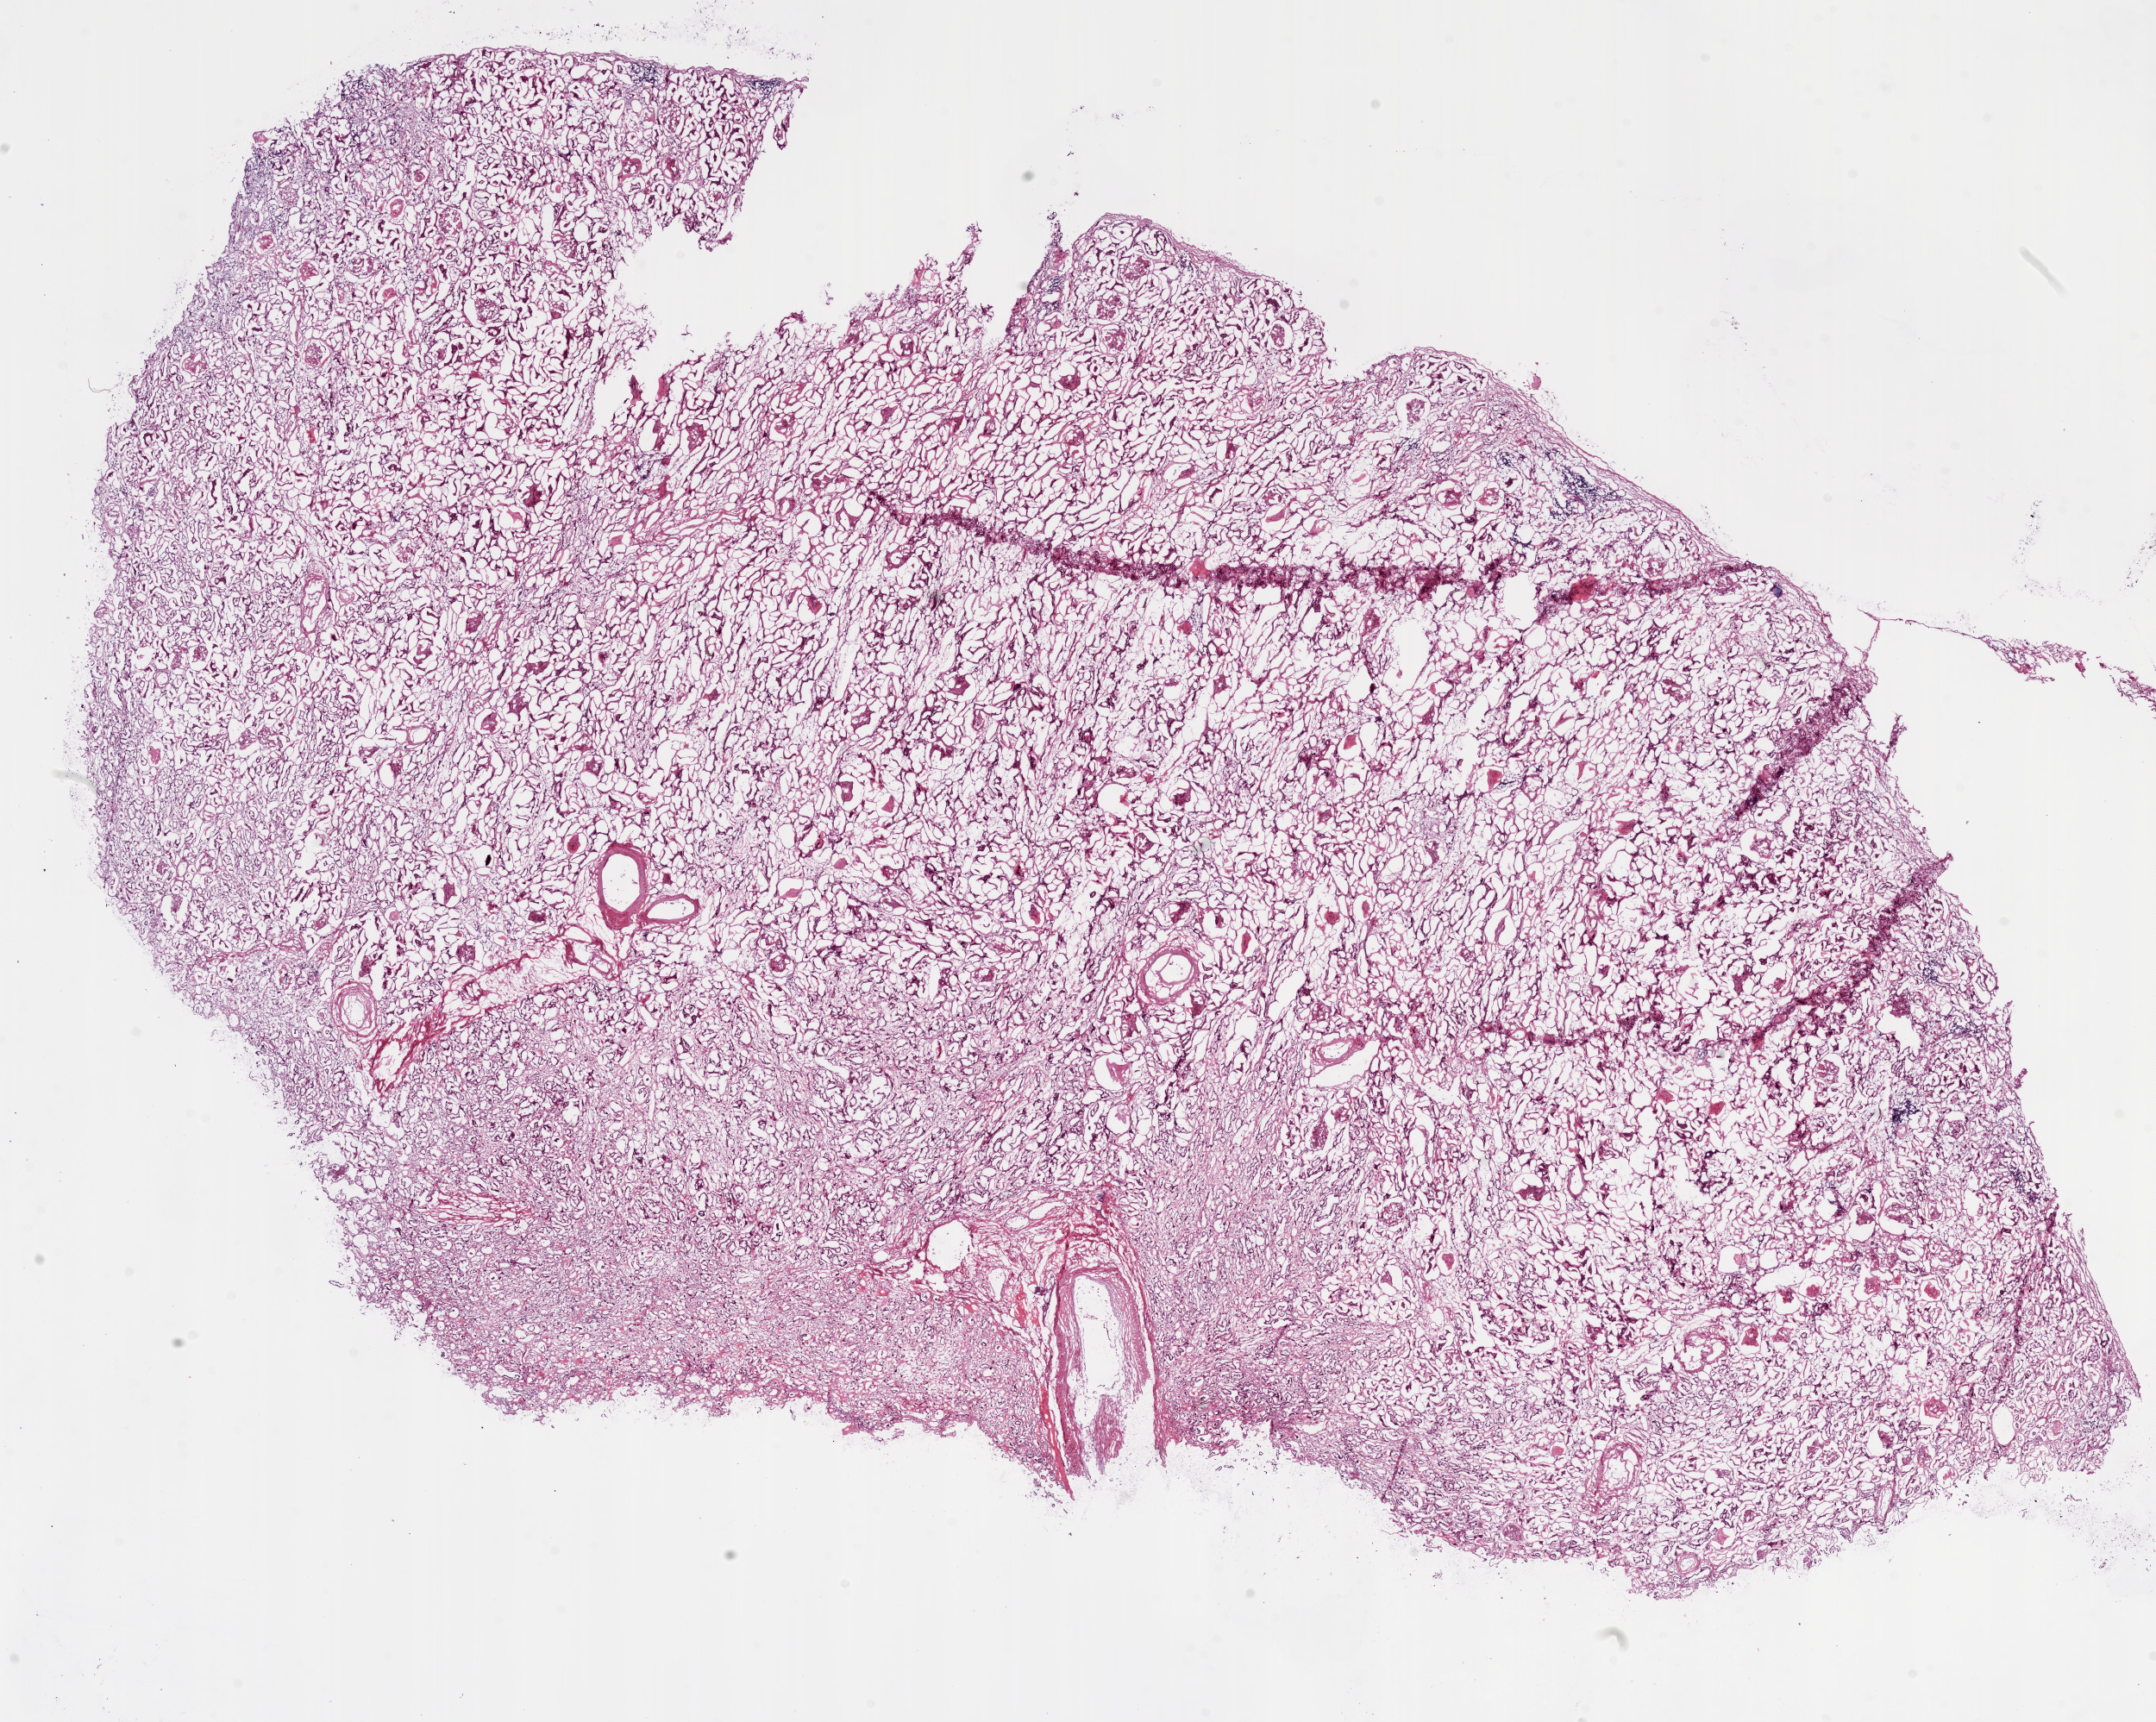
Digitized H&E-stained tissue section (whole slide) — a low-resolution overview of the entire scanned area, about 20.1 x 16.0 mm, frozen section, solid tissue normal (non-tumour tissue) sample from the kidney. Patient: male, age at initial diagnosis 48 years.
- this section: solid tissue normal sample (biorepository sample class)
- patient diagnosis: Clear cell adenocarcinoma, NOS